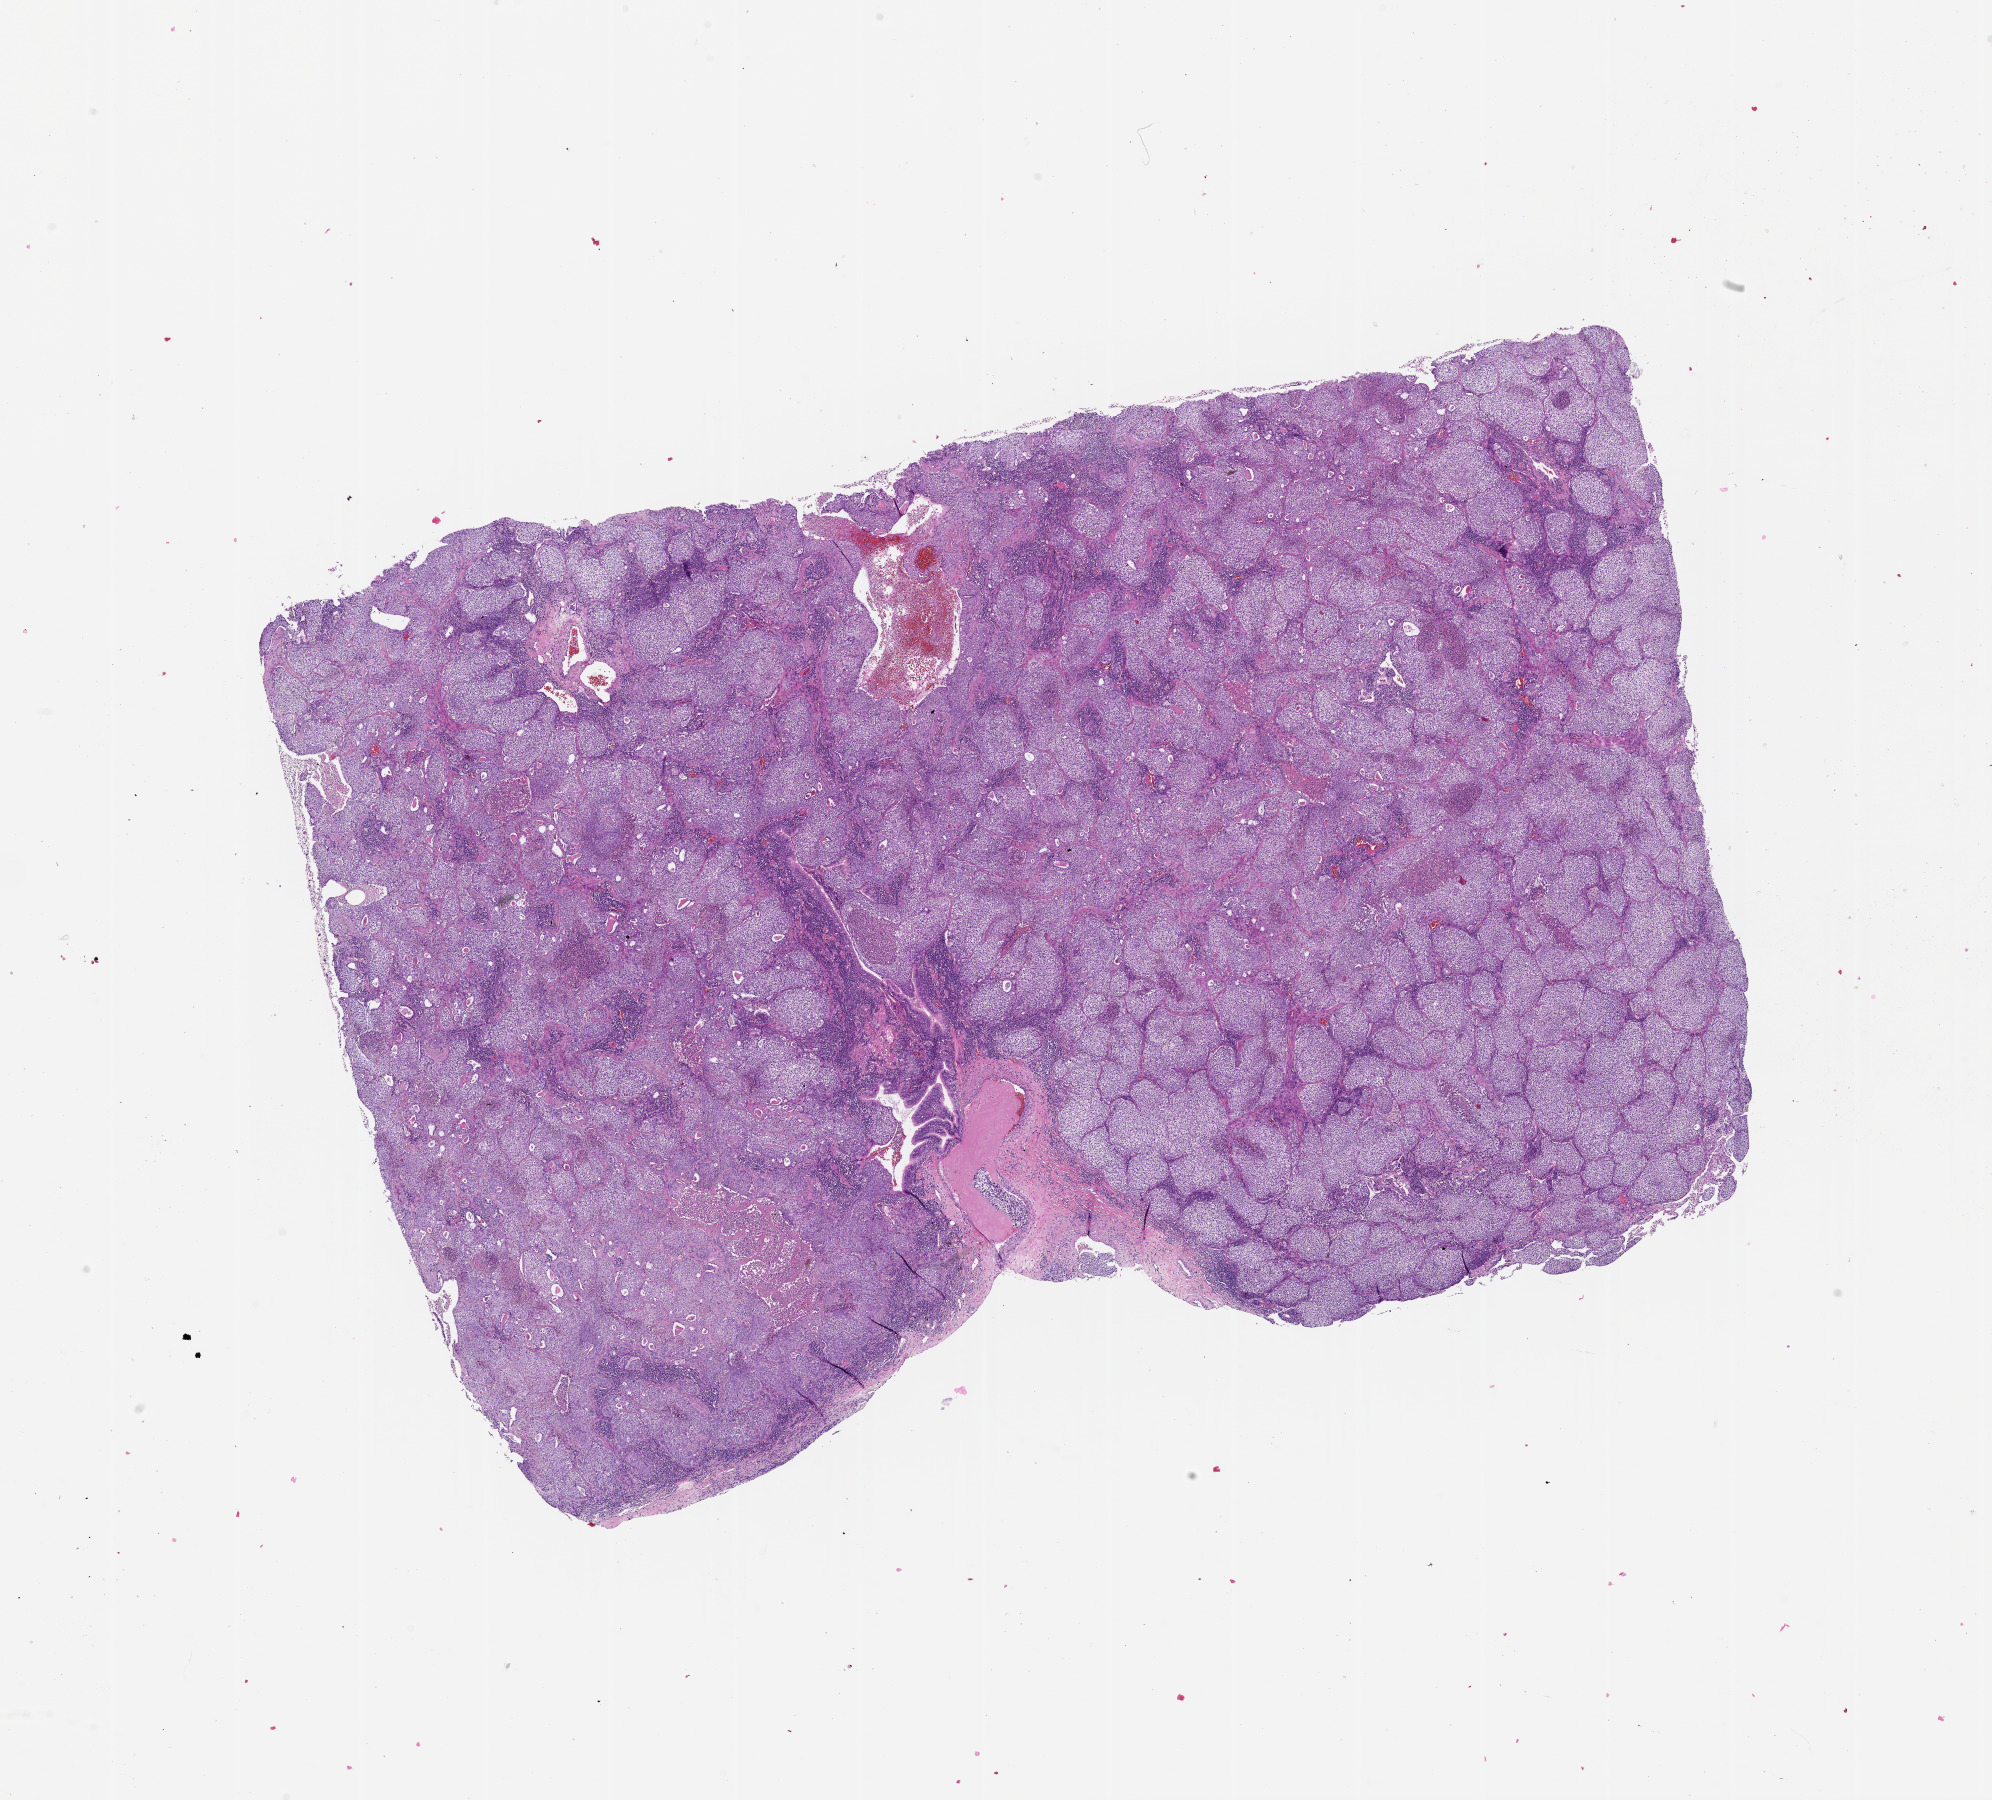
Whole-slide histology image, H&E, low-resolution overview of the scanned area, about 16.0 x 14.5 mm (from a 20x scan). Tumour tissue sample, lung. Male, 60 y/o.
* patient diagnosis (cohort enrolment): squamous cell carcinoma (lung)